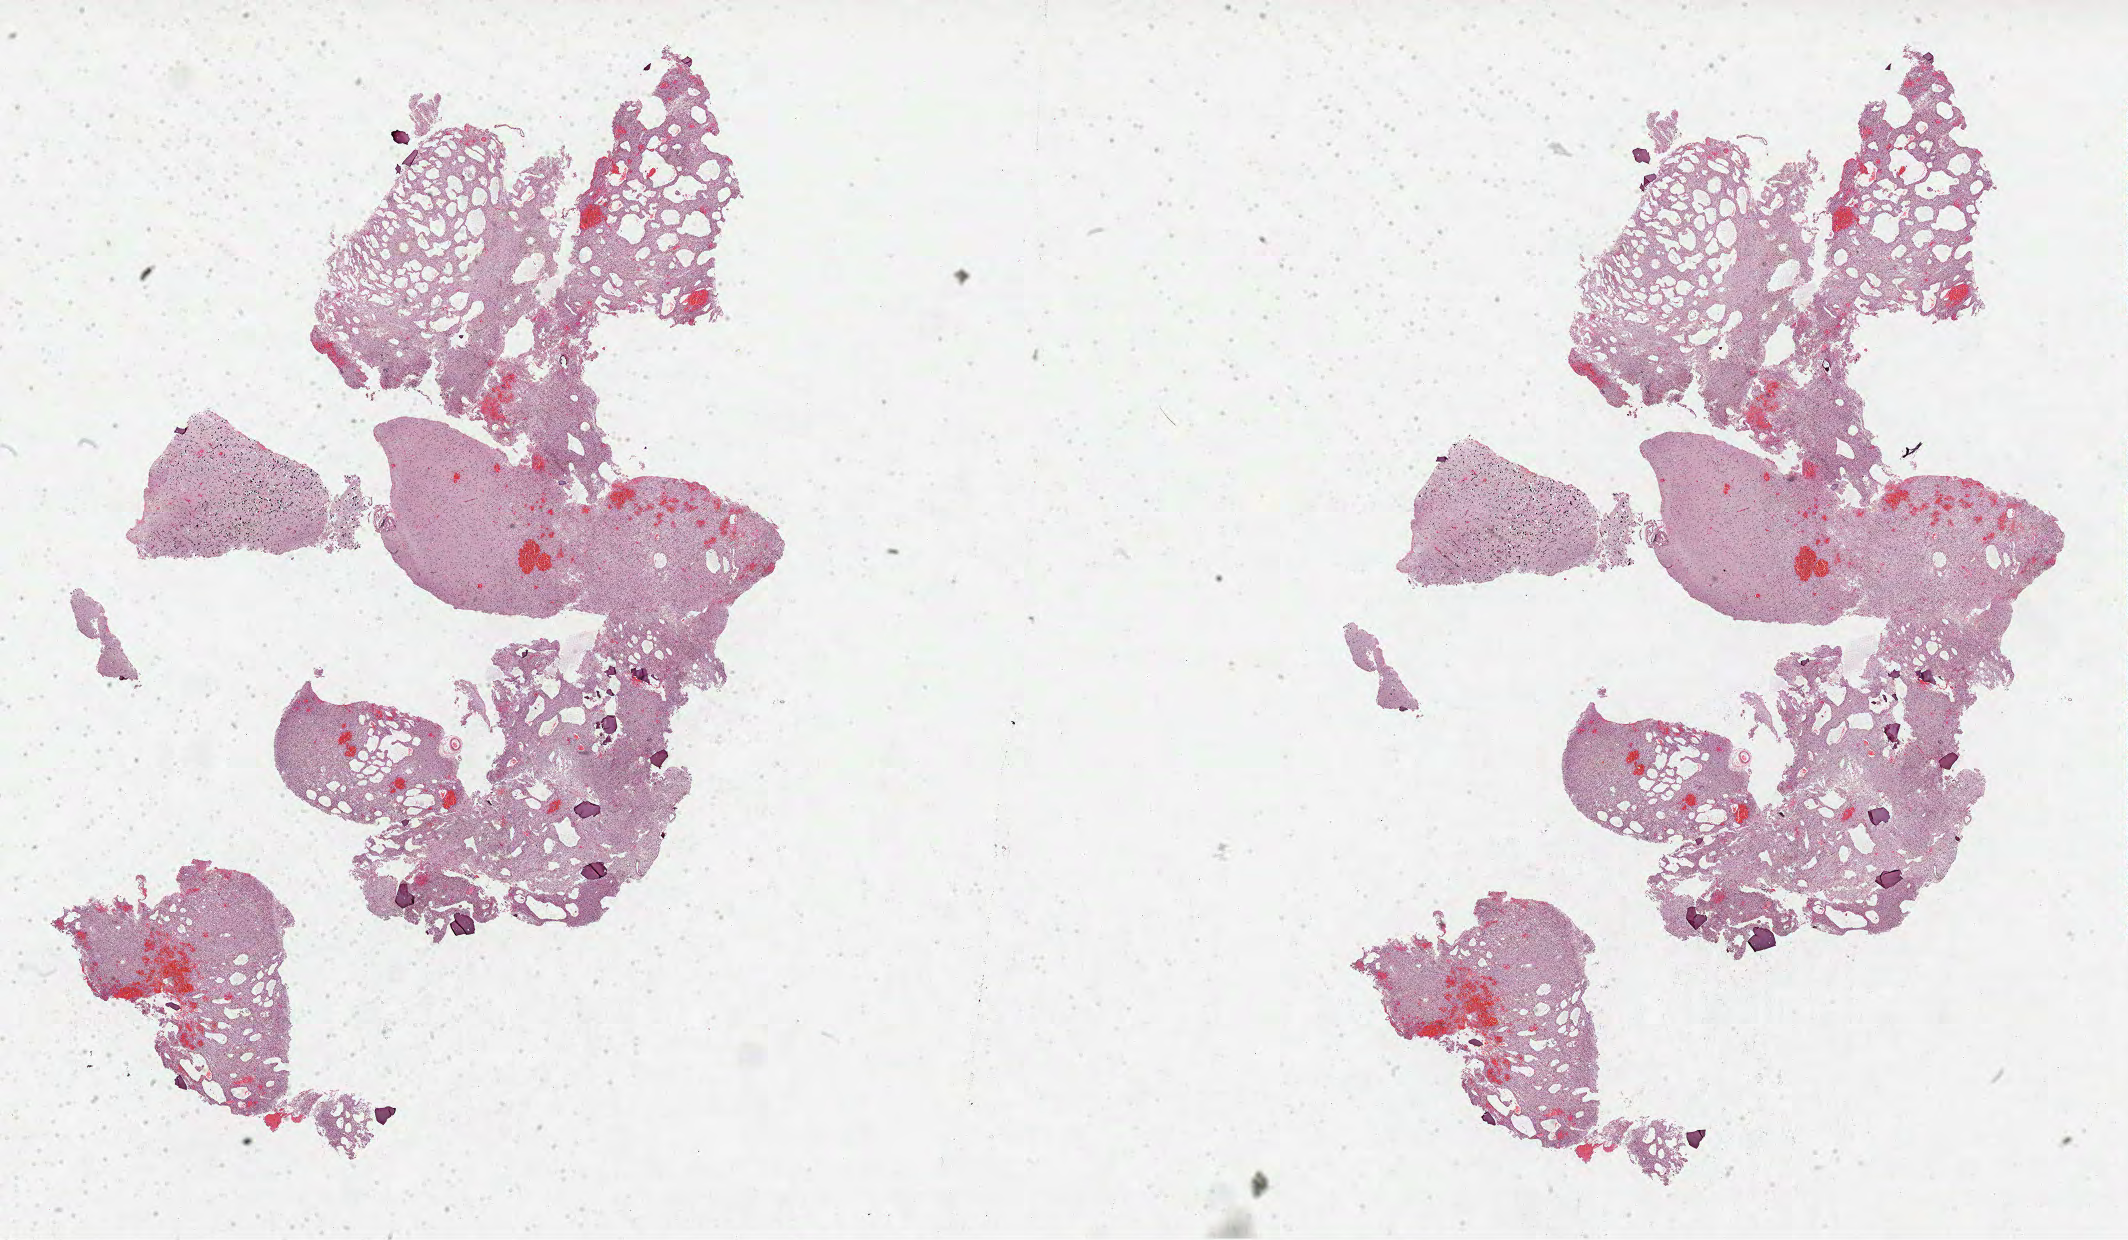
Whole-slide histology image, H&E-stained — shown as a low-resolution overview of the whole scanned area (about 34.3 x 20.0 mm, acquisition: 40x scan). Formalin-fixed paraffin-embedded (FFPE) diagnostic section. Sample: primary tumour, brain. Patient: female, age at initial diagnosis 49 years. Histologic grade: G2 (moderately differentiated).
Laterality: right. Pathologic diagnosis: Mixed glioma (cerebrum).